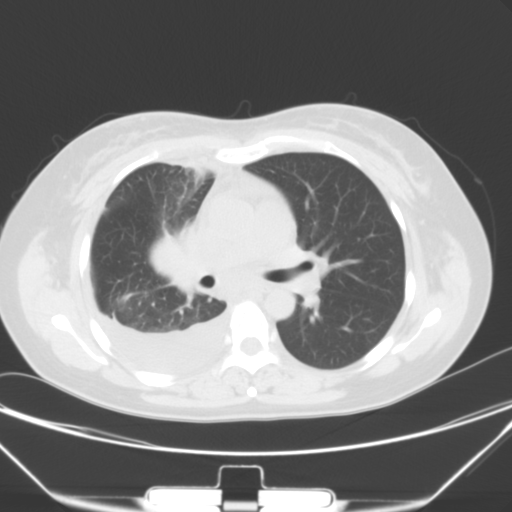
Chest CT, one axial slice; position 19 of 40 along the scan axis; 120 kVp; lung window (W 1500 / L -600 HU); 512 × 512 image matrix, field of view 352 × 352 mm. Female patient, age 36 years. Case-level facts recorded for this patient, not image findings: clinical TNM (as recorded): T1b N2 M0; histopathological grade: G3.
Outlined on this slice (rectangle marked by the reading radiologist):
- lung tumour (recorded histology: adenocarcinoma): bounding box (x1, y1, x2, y2) in pixels: (152, 225, 203, 297)